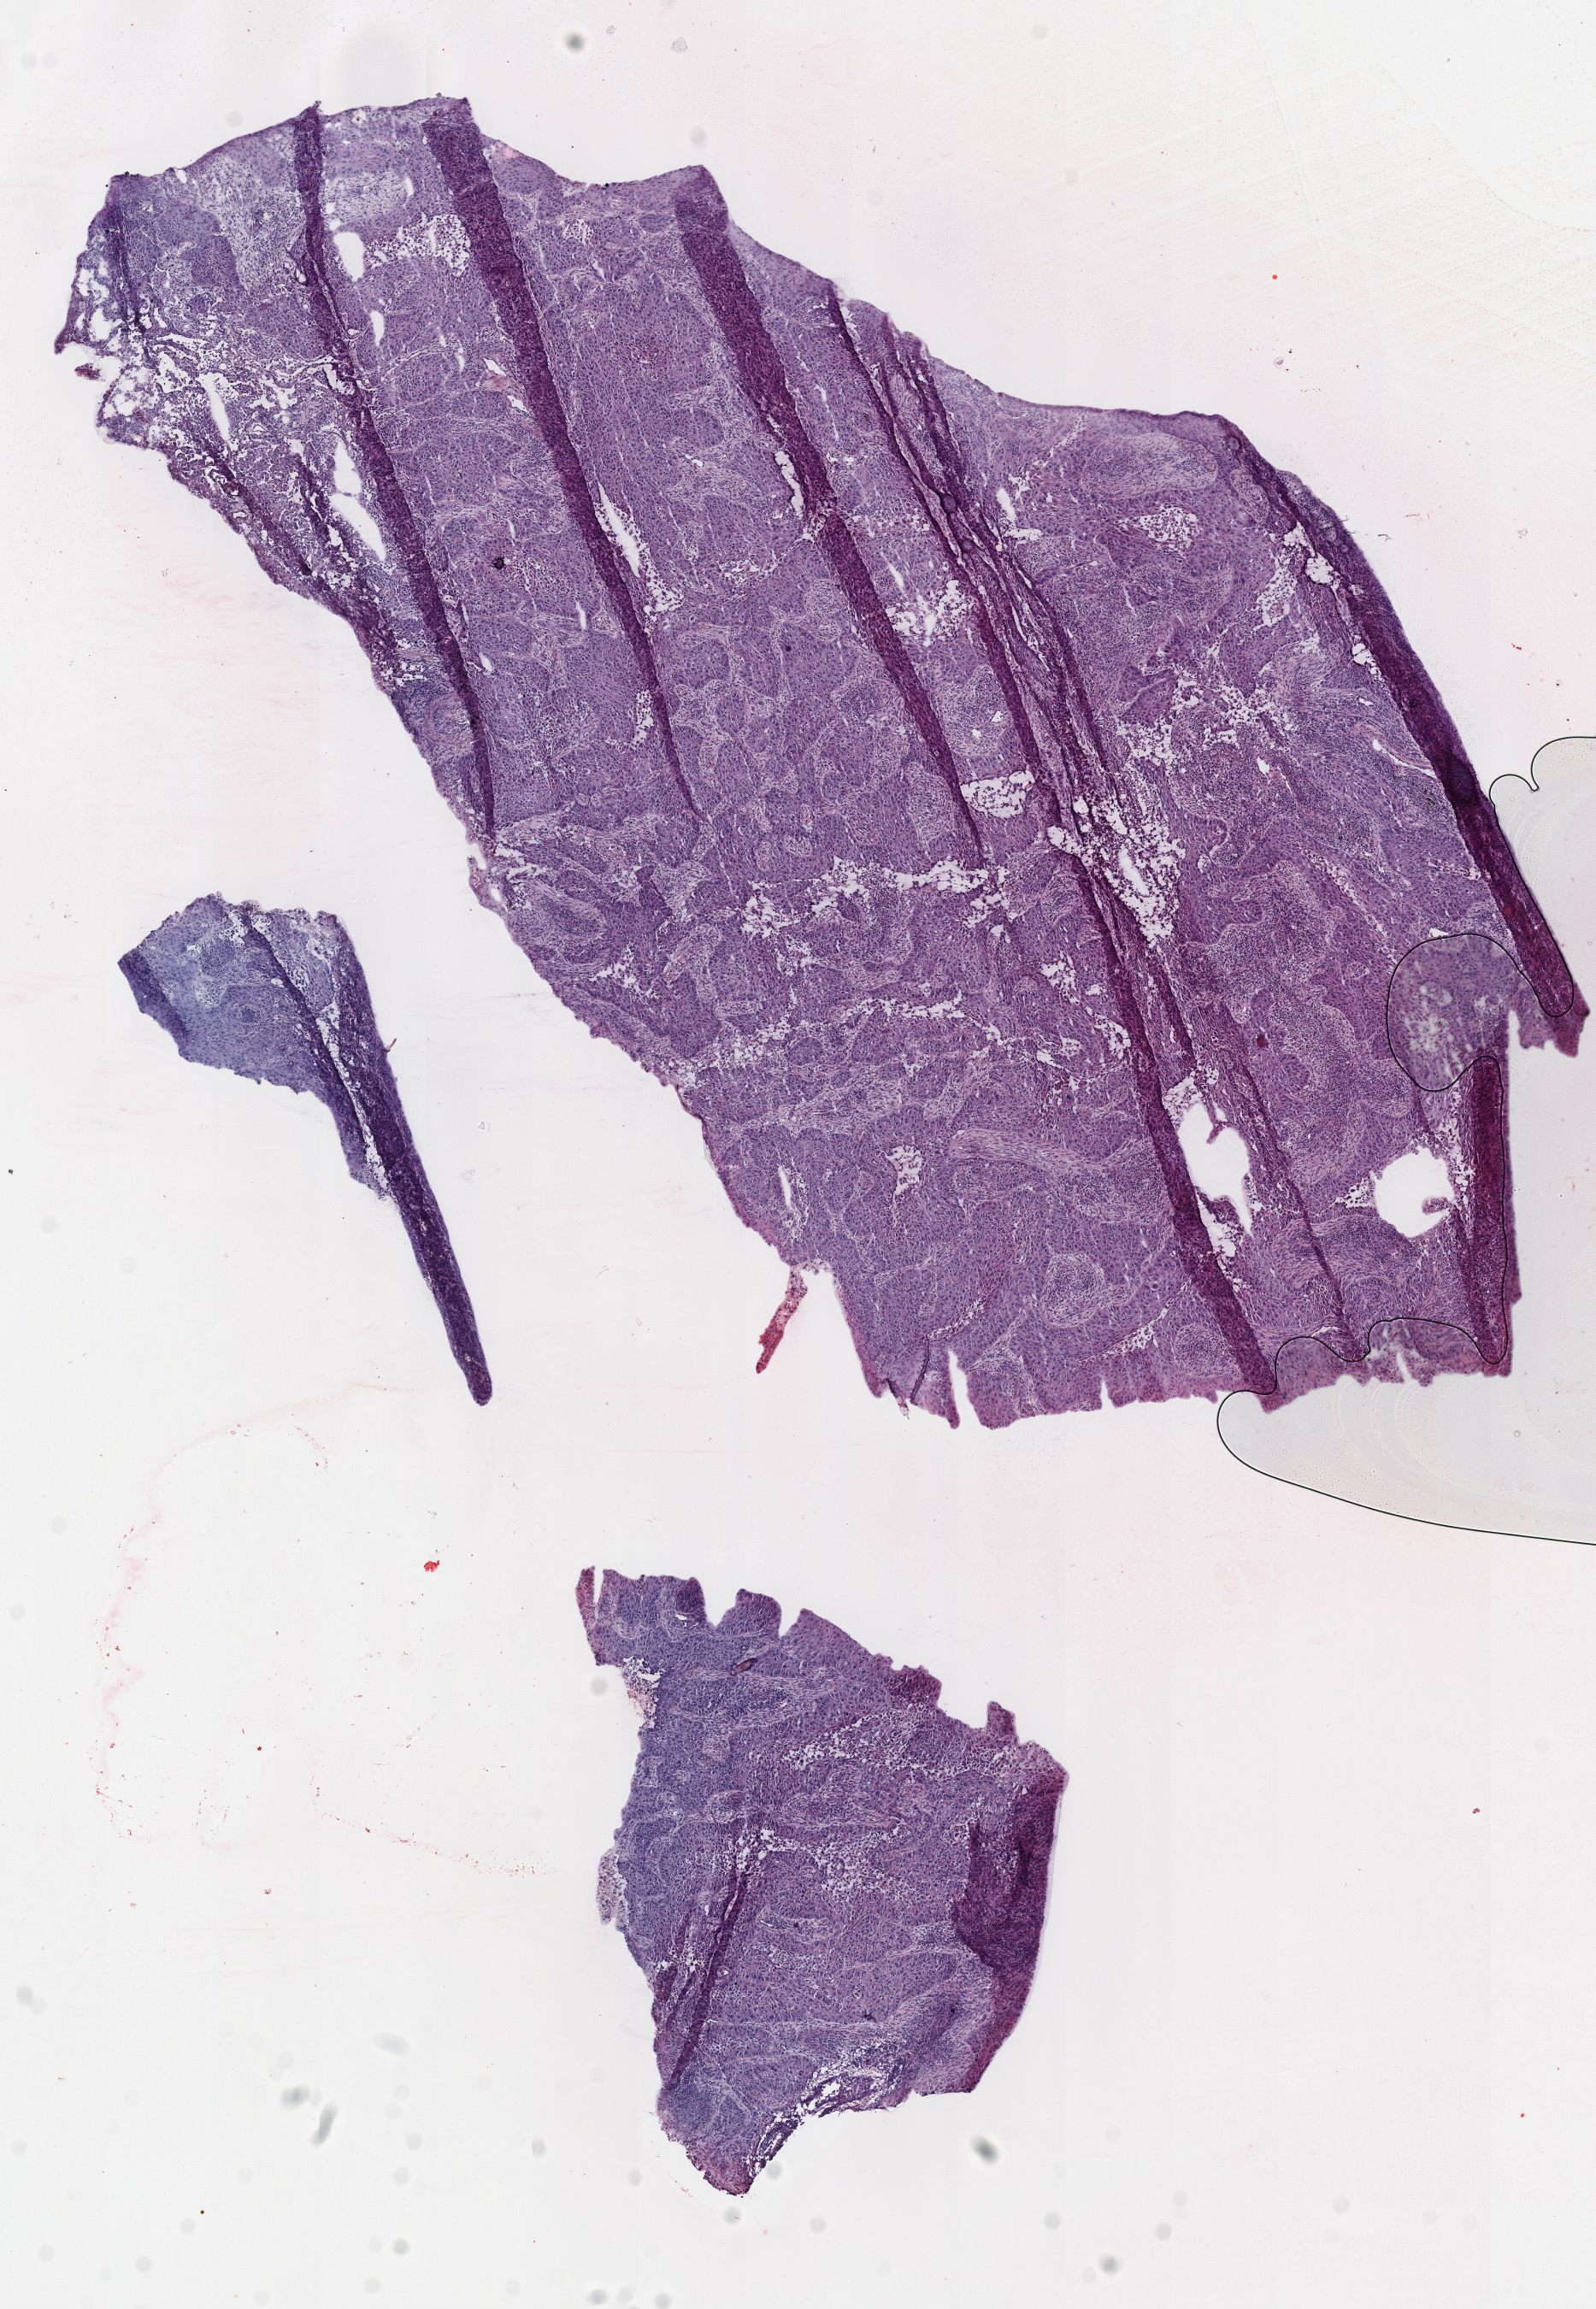
Hematoxylin and eosin (H&E) stained whole-slide image, shown as a low-resolution overview of the whole scanned area (about 7.3 x 10.6 mm, from a 40x scan); frozen section; lung, primary tumour sample. Female, age 68 years at initial diagnosis. Pathologist review of this section (percent, as recorded): tumour cells 90%, tumour nuclei 75%, normal cells 1%, stromal cells 7%, necrosis 2%. Inflammatory infiltration, as recorded: lymphocyte infiltration 18%, monocyte infiltration 2%.
• AJCC pathologic stage: IB (7th edition)
• pathologic diagnosis: Squamous cell carcinoma, NOS (lower lobe, lung)
• laterality: right